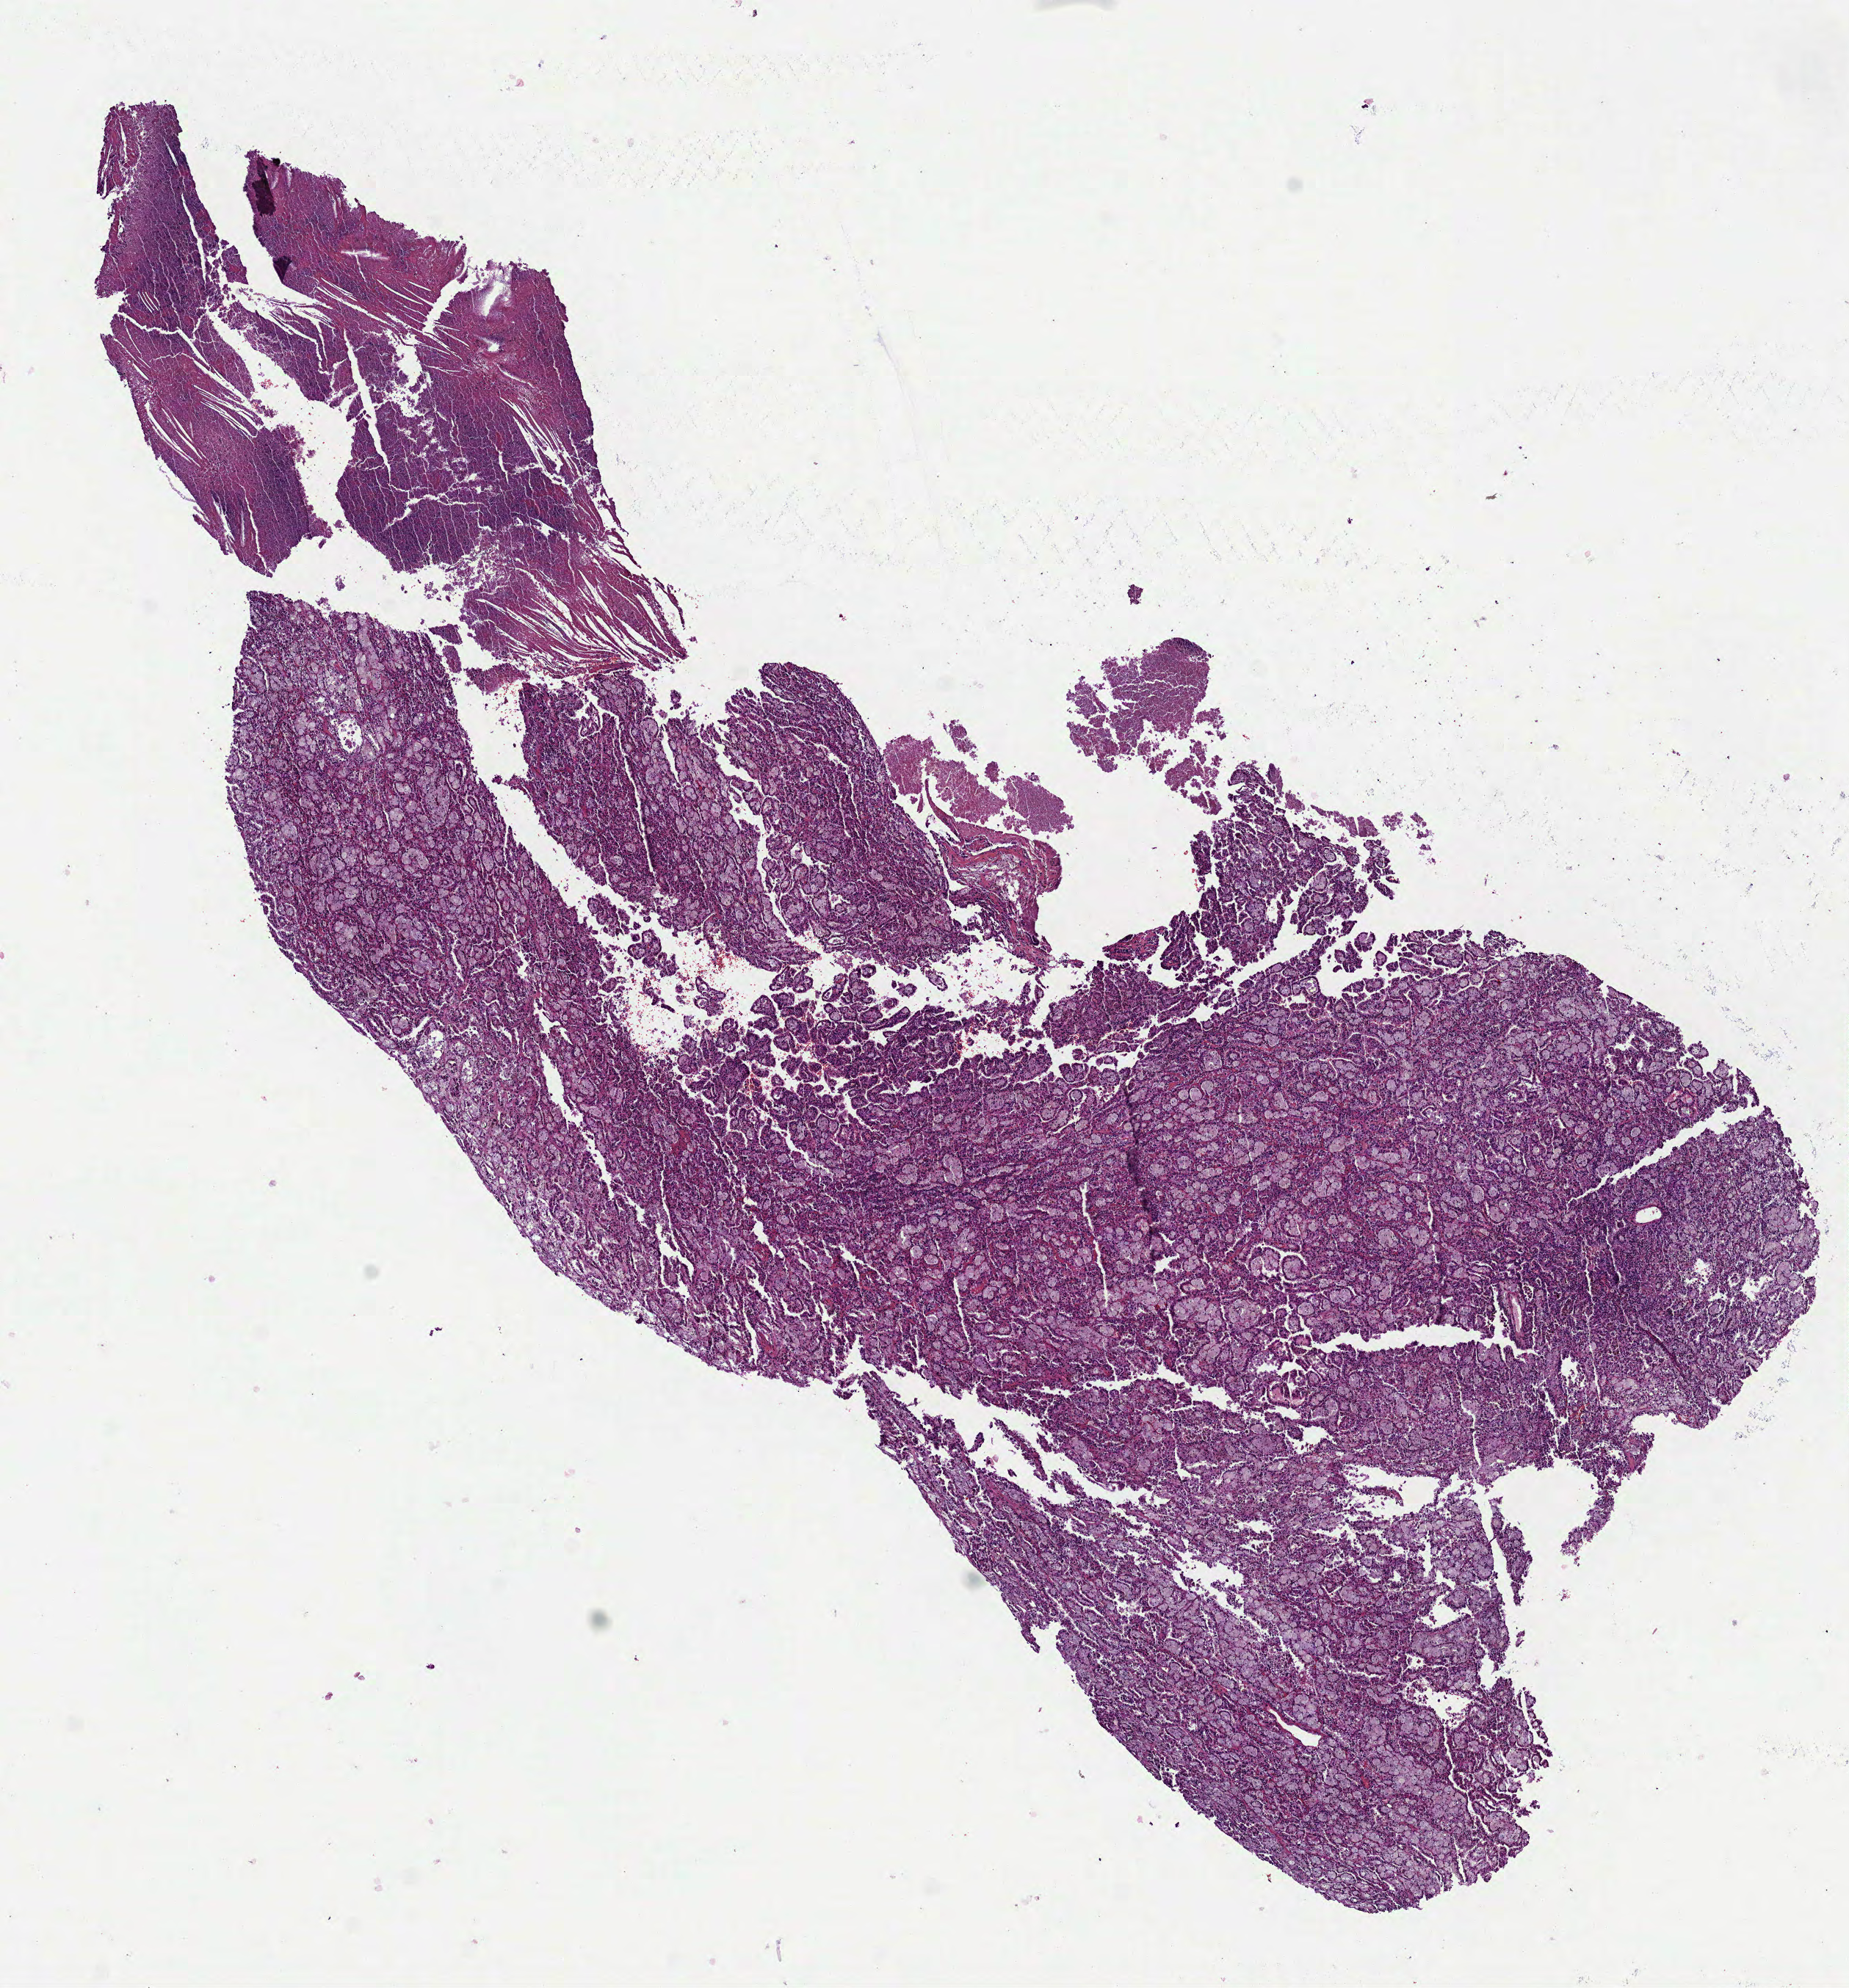
Digitized H&E tissue section (whole slide), low-resolution overview of the scanned area, about 10.2 x 10.9 mm (from a 40x scan), FFPE section, sample: primary tumour, kidney. Patient: female, age at initial diagnosis 65 years.
AJCC pathologic stage: II (7th edition). Laterality: right. Histologic diagnosis: Papillary adenocarcinoma, NOS.